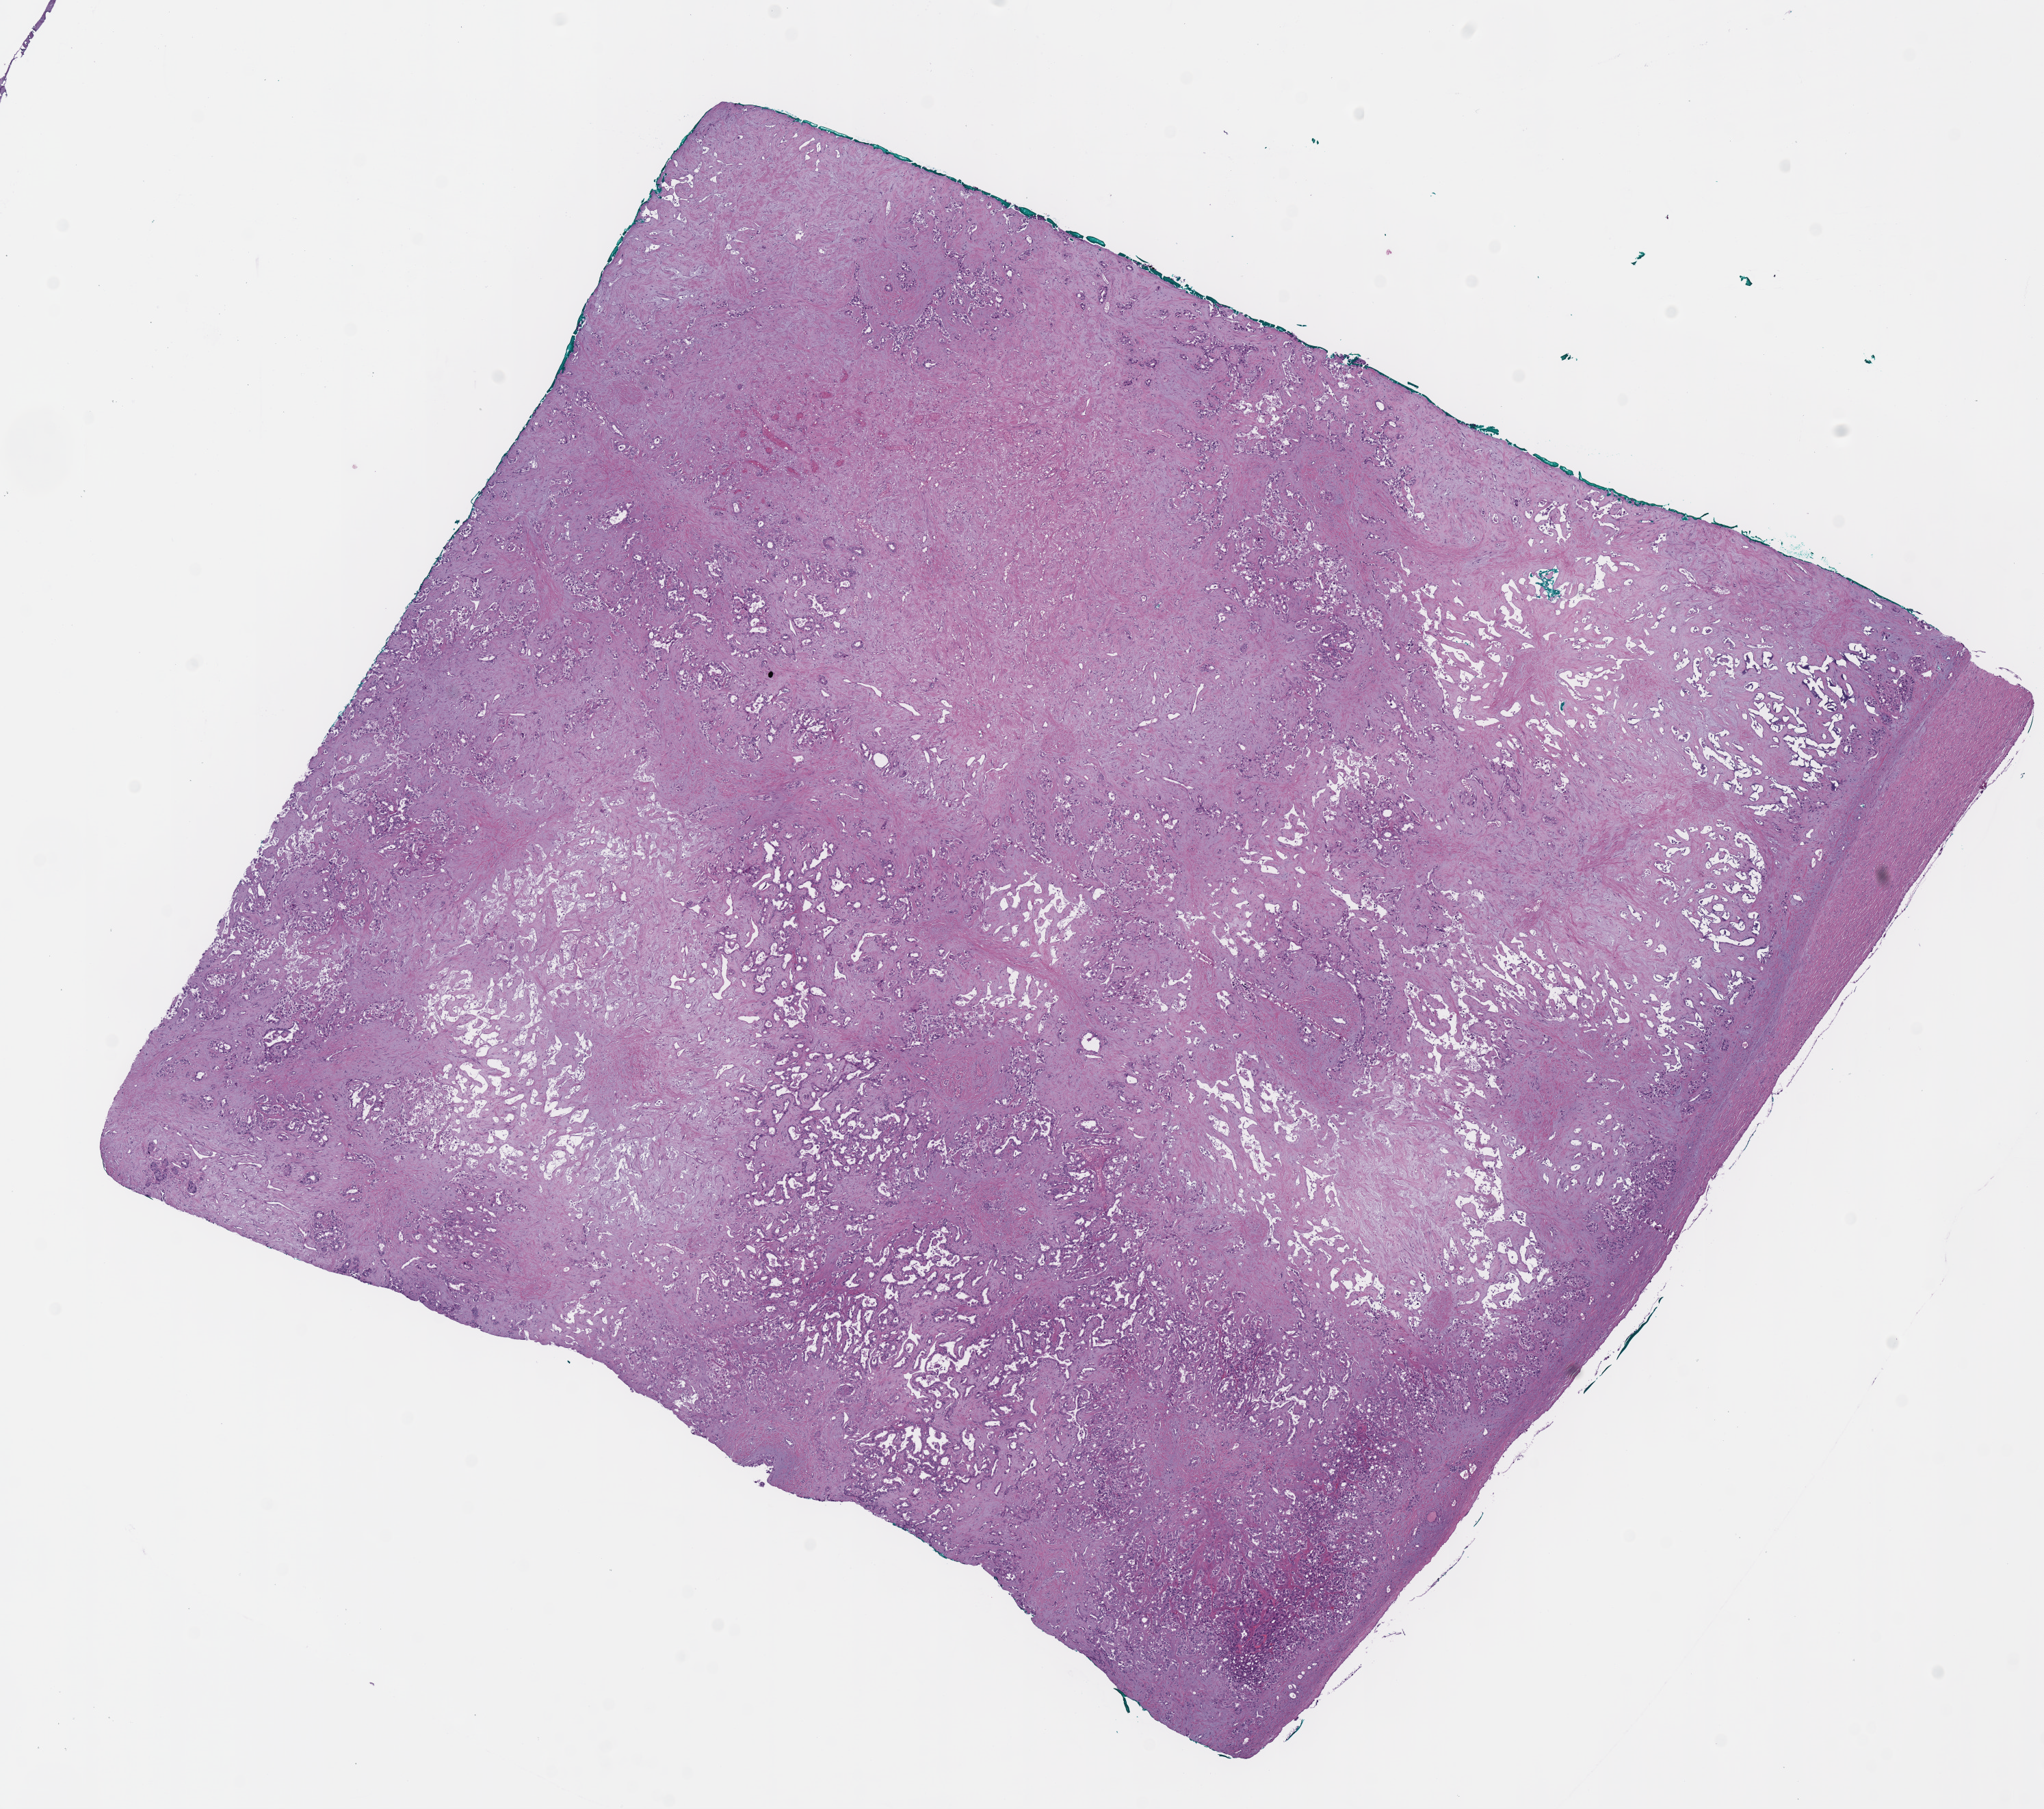
Digitized Hematoxylin and eosin (H&E) stained tissue section (whole slide) — a low-resolution overview of the entire scanned area, about 11.7 x 10.4 mm, FFPE section, liver, primary tumour sample. Patient: female, age at initial diagnosis 76 years. Histologic grade: G2 (moderately differentiated).
- TNM: T2 NX M0
- histologic diagnosis: Hepatocellular carcinoma, fibrolamellar
- AJCC pathologic stage: II (7th edition)